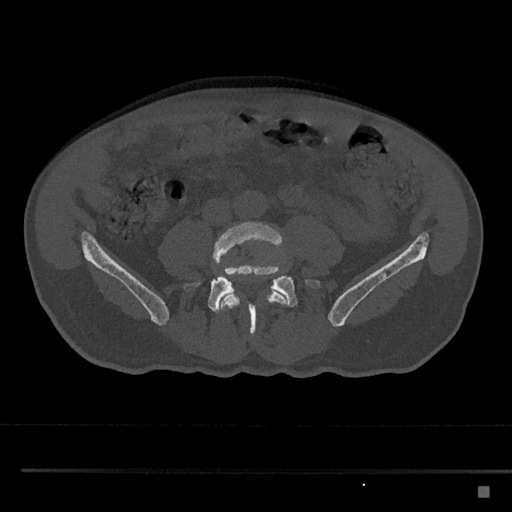
CT including the spine, one axial slice. Slice 605 of 797 in the series (ordered by position). Reconstruction kernel Br40s/3. Bone window (W 1800 / L 400 HU). 0.5 mm slice thickness. 512 × 512 image matrix. Patient: male, 59 years. Case-level facts recorded for this patient, not image findings: primary cancer: prostate.
Outlined on this slice (semi-automatic segmentation, software-assisted and operator-edited):
- L4 vertebra: bounding box [x1, y1, x2, y2] px = [212, 222, 289, 325]
- L5 vertebra: [182, 261, 322, 338]